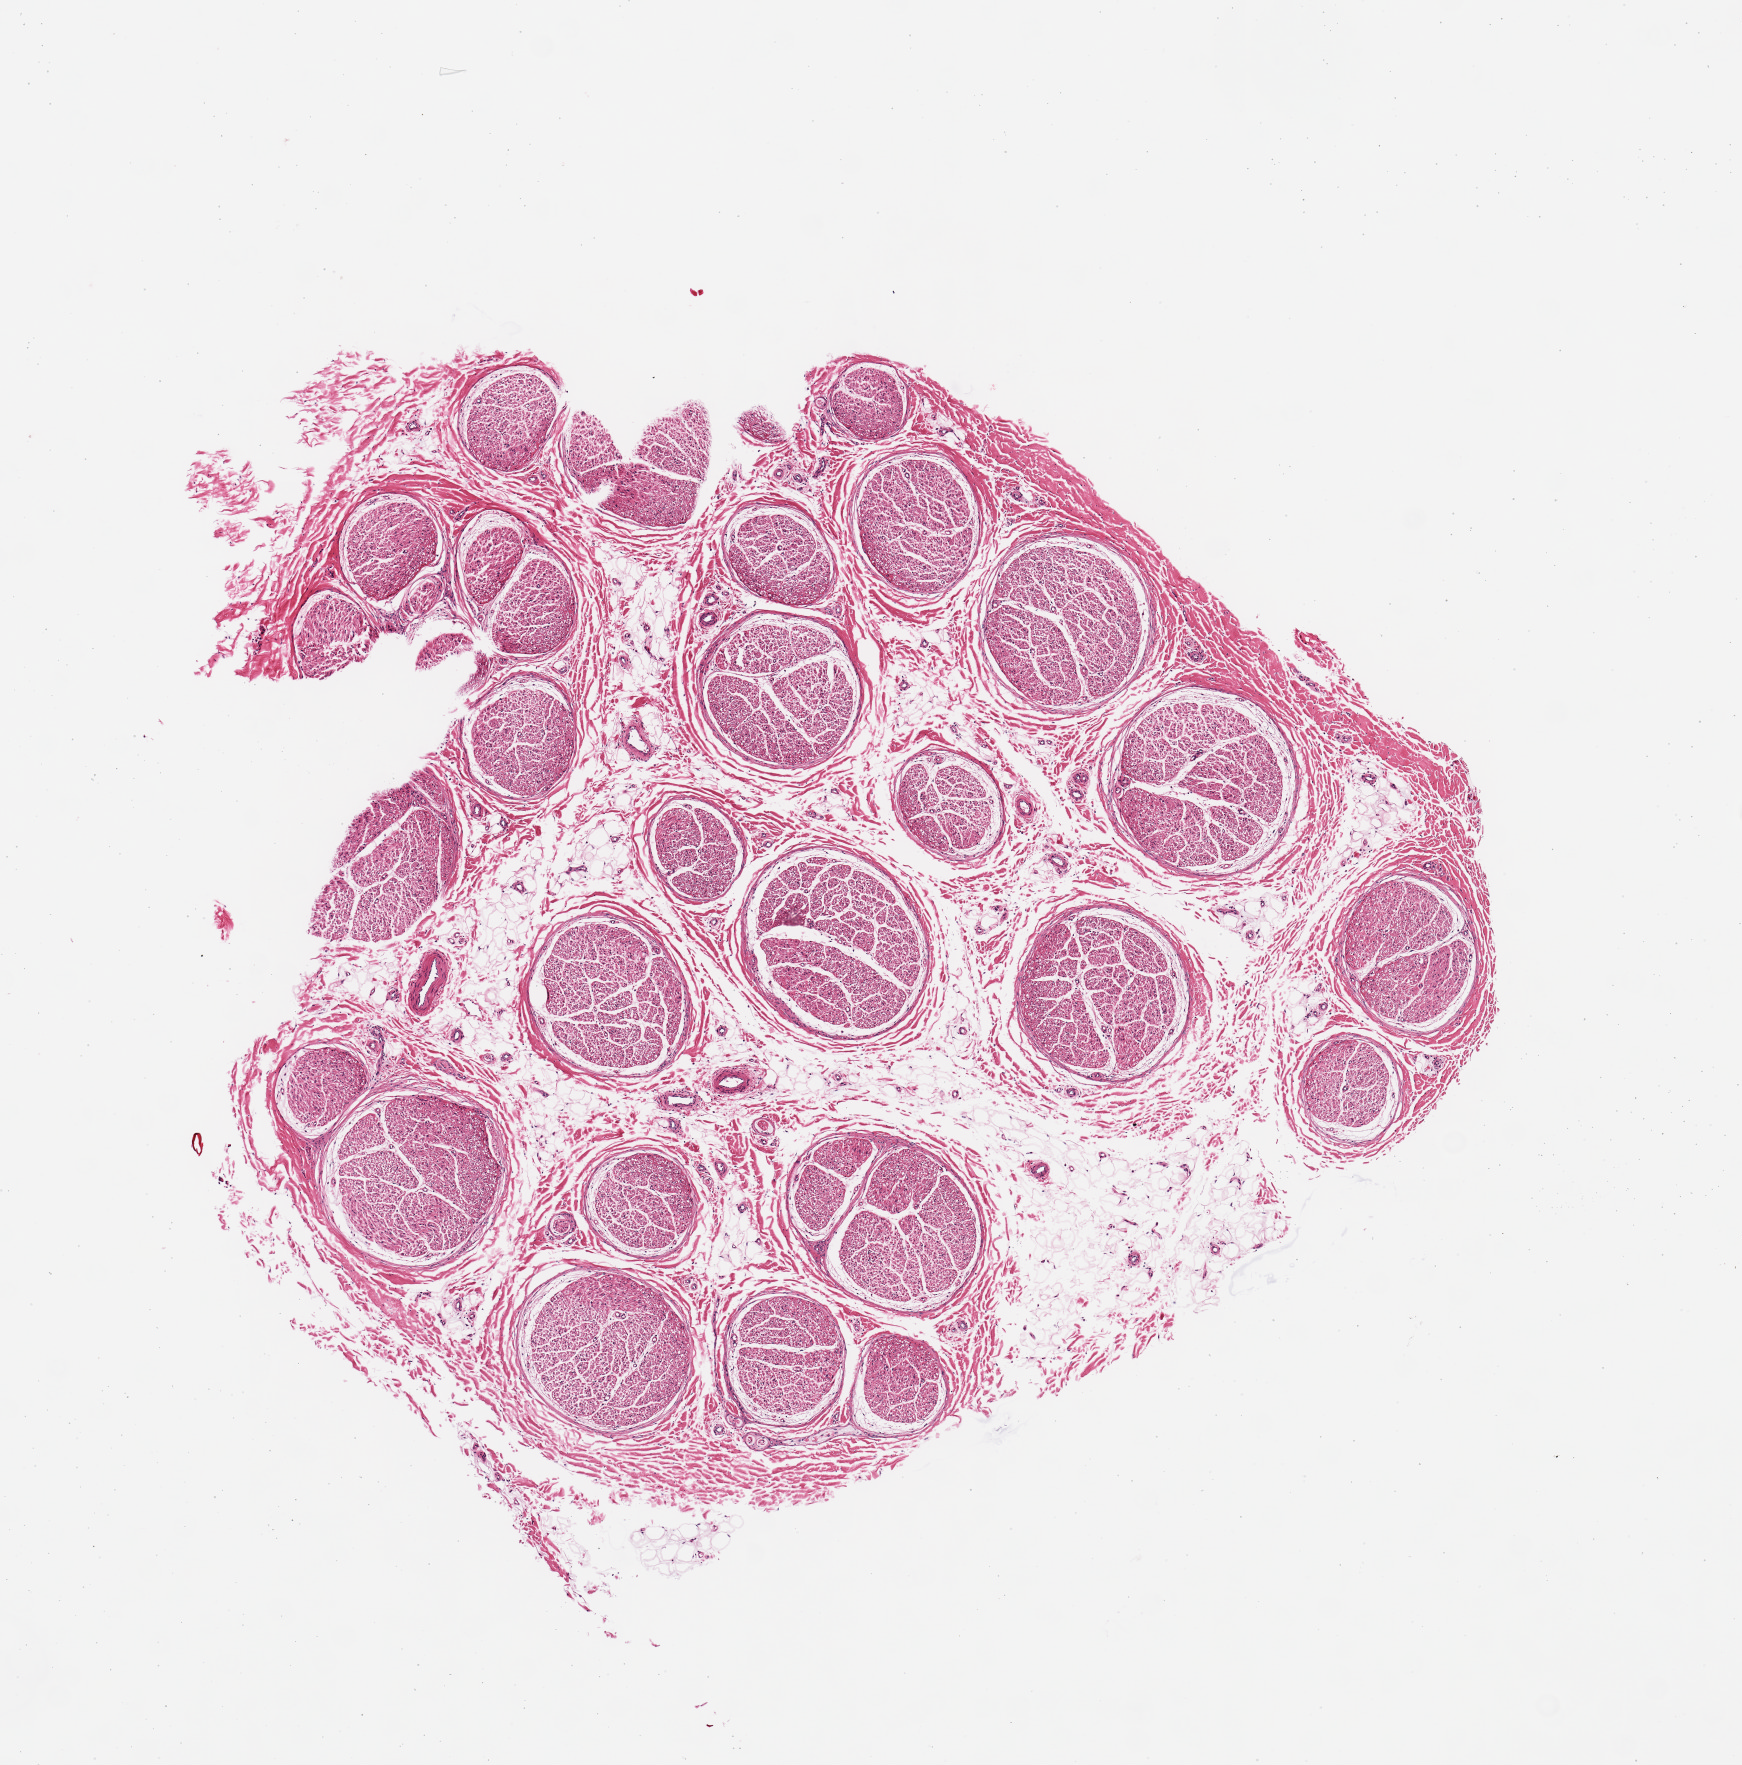
H&E whole-slide image — a low-resolution overview of the entire scanned area, about 6.9 x 7.0 mm (from a 20x scan); PAXgene-fixed, paraffin-embedded tissue; section of tibial nerve (target tissue); donor tissue sample. Donor: female.
Reviewer comment on this tissue sample: 1 piece; nerve not artery; 20% internal fat.